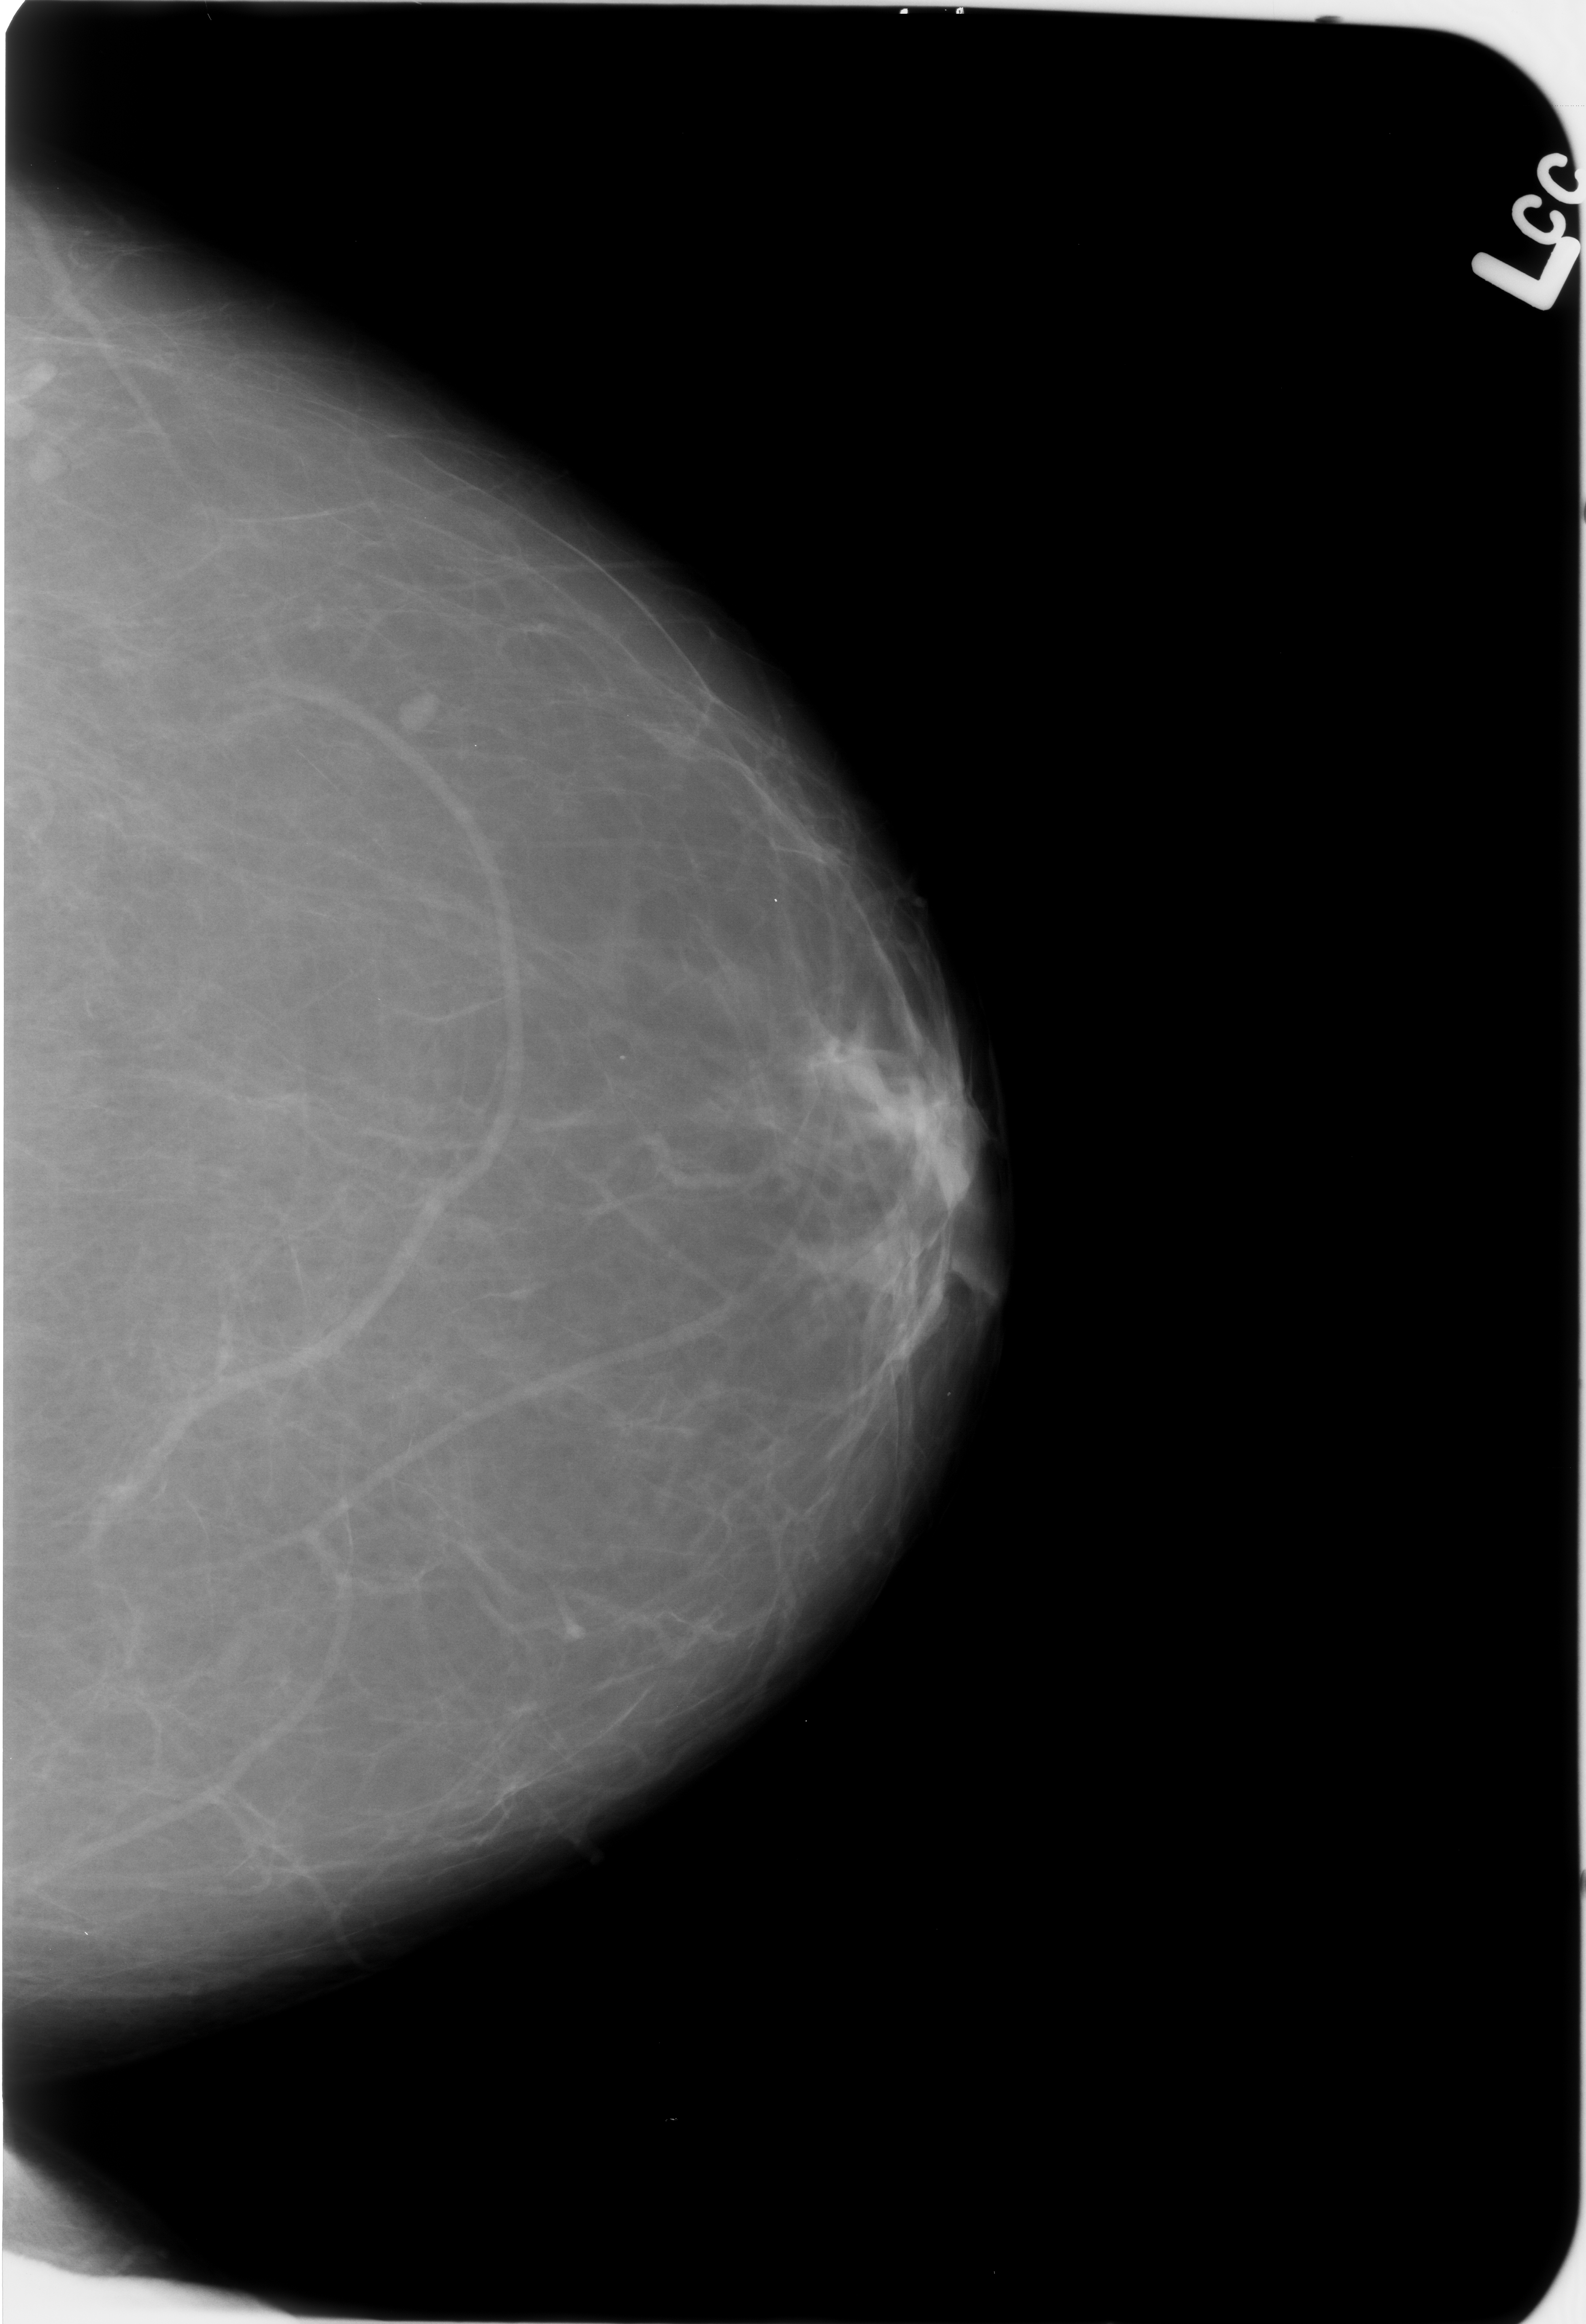
Mammogram (digitized film); left breast; craniocaudal (CC) view; BI-RADS breast density category 1 (scale 1–4); 1586 × 2324 image matrix.
Expert-marked regions of interest on this image (one box per marked abnormality):
- Finding 1 of 3: mass, shape lymph node, margins circumscribed; BI-RADS assessment category 2; outcome (as recorded, no biopsy): benign without callback (not worked up further): bounding box <0,368,36,460> (left, top, right, bottom; pixels)
- Finding 2 of 3: mass, shape lymph node, margins circumscribed; BI-RADS assessment category 2; subtlety rating 4 on a 1 (subtle) to 5 (obvious) scale; outcome (as recorded, no biopsy): benign without callback (not worked up further): <26,441,66,486>
- Finding 3 of 3: mass, shape lymph node, margins circumscribed; BI-RADS assessment category 2; subtlety rating 4 on a 1 (subtle) to 5 (obvious) scale; benign; no additional work-up was recommended (outcome (as recorded, no biopsy): benign without callback): <390,679,447,743>